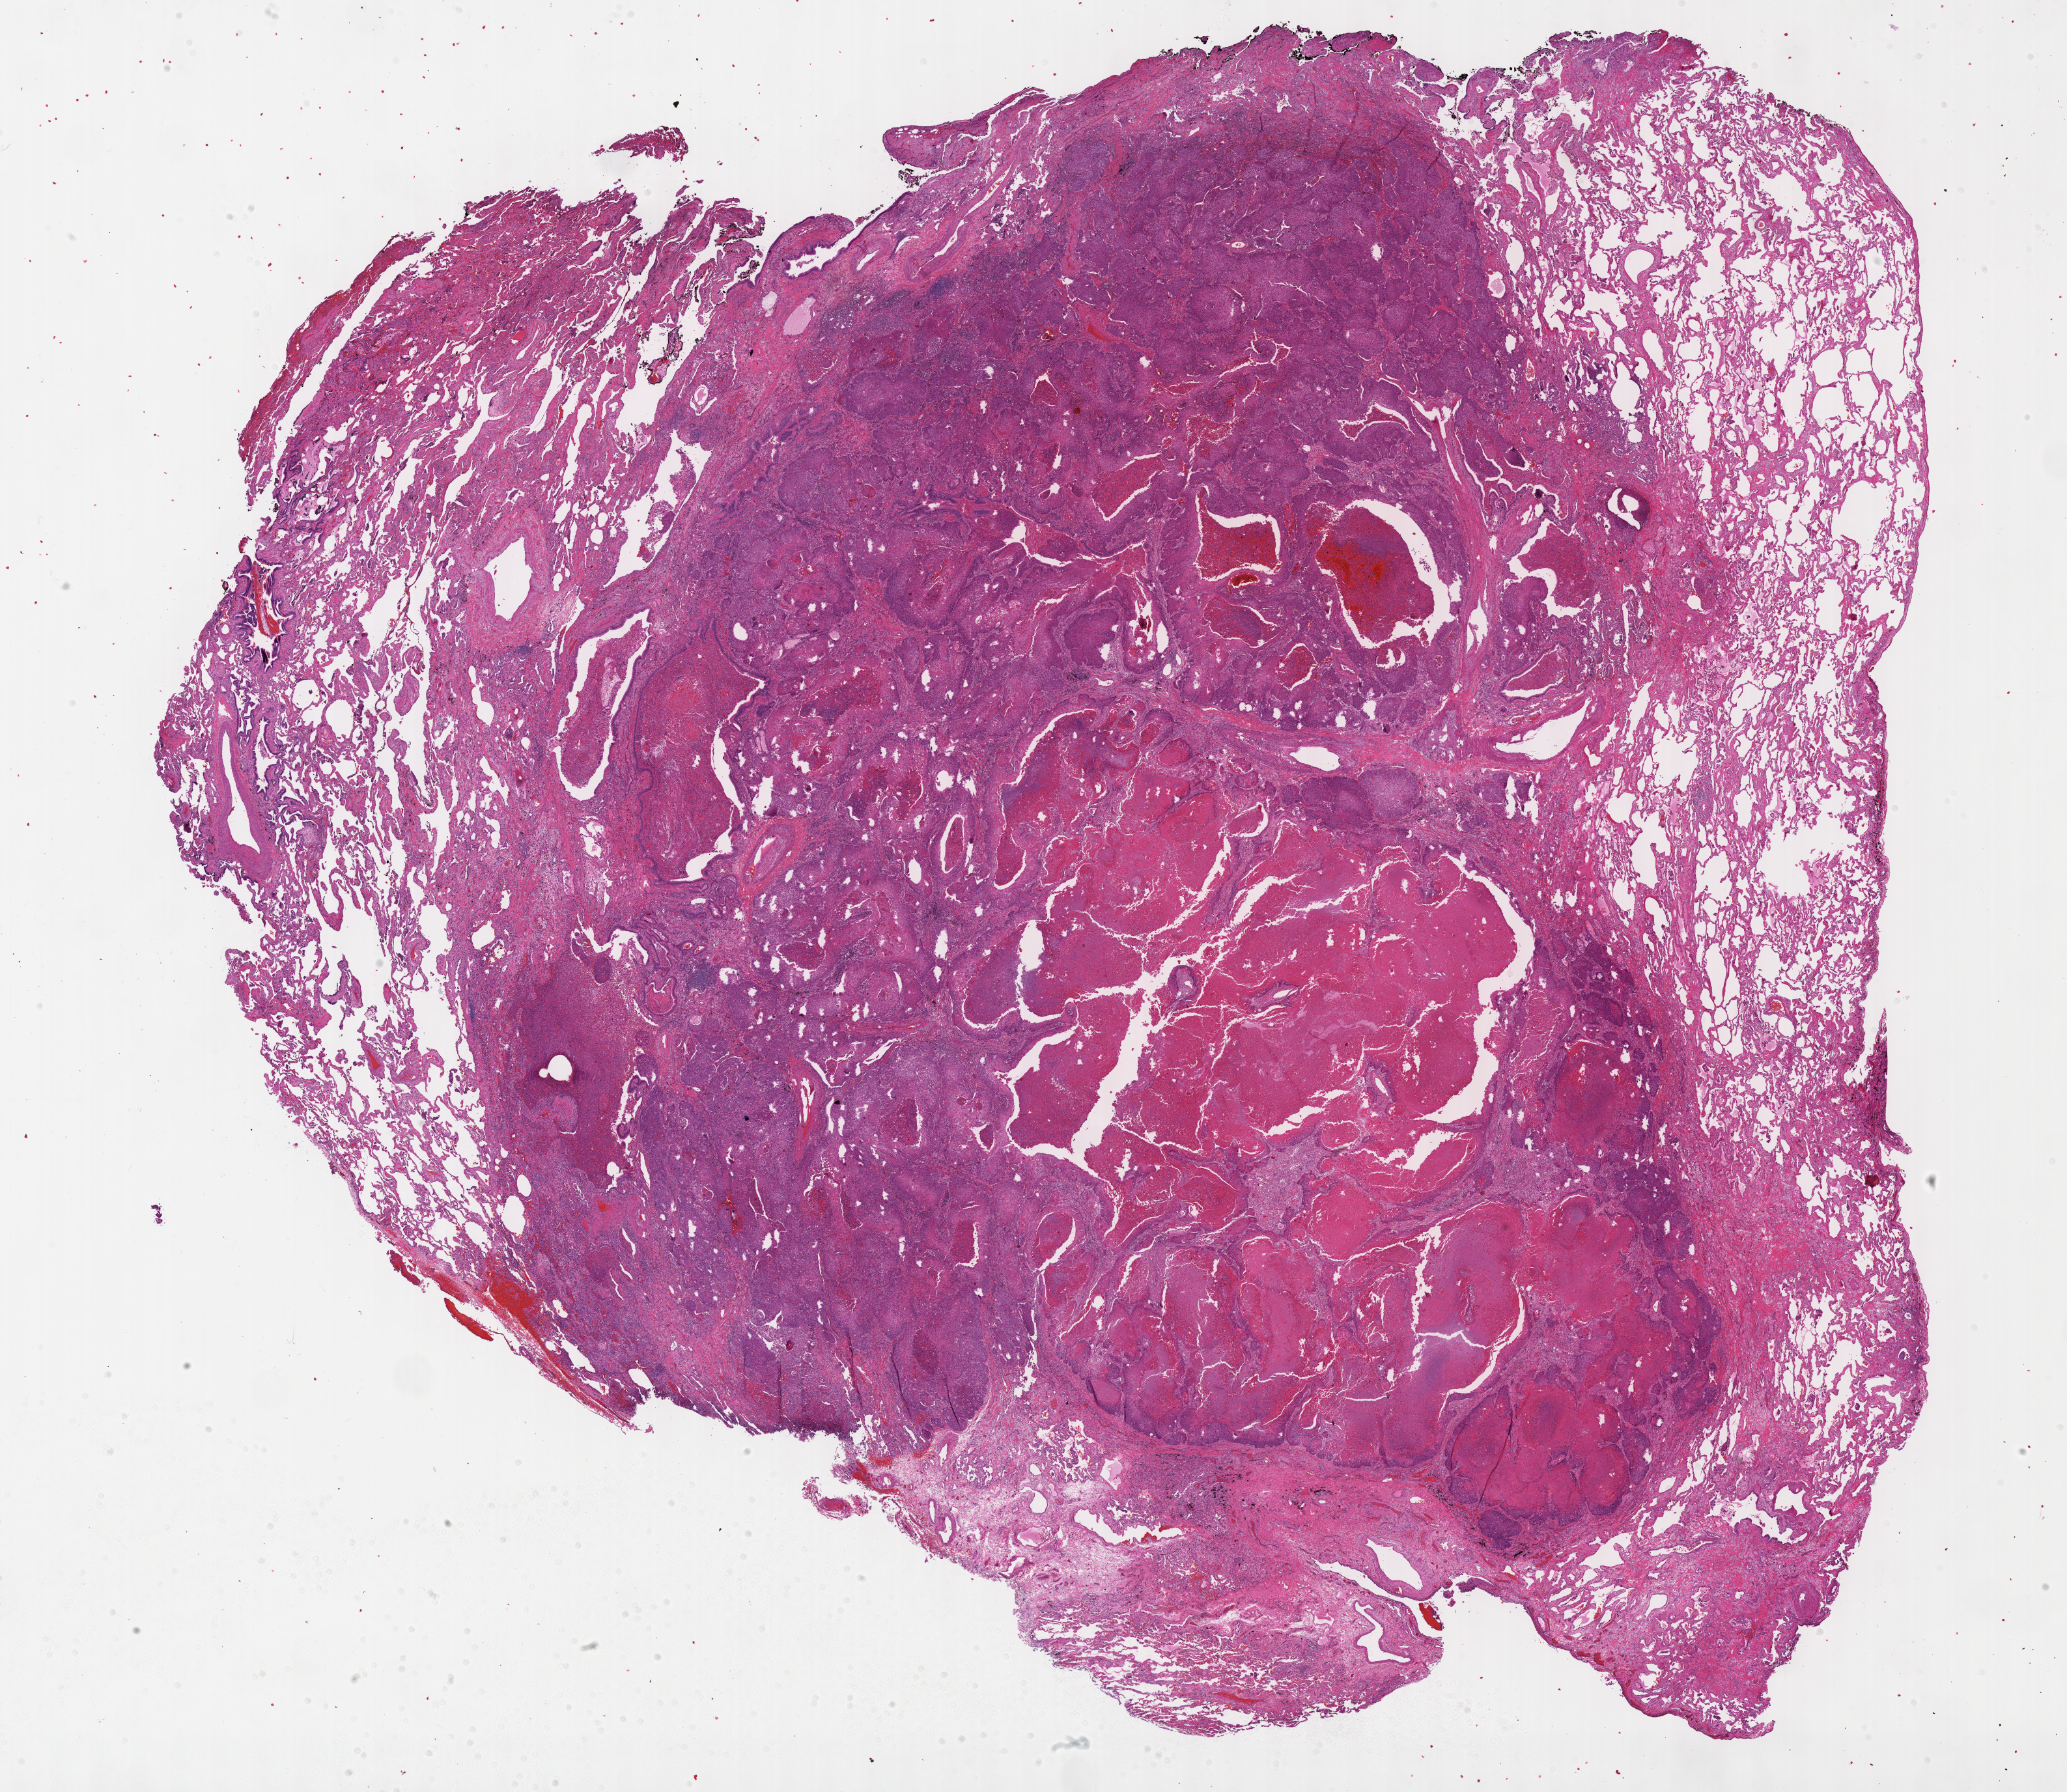
H&E-stained whole-slide image, shown as a low-resolution overview of the whole scanned area (about 25.7 x 22.3 mm); formalin-fixed paraffin-embedded (FFPE) diagnostic section; sample: primary tumour, lung. Male, age 67 years at initial diagnosis.
* laterality: right
* AJCC pathologic stage: IIA (7th edition)
* diagnosis: Squamous cell carcinoma, NOS (lower lobe, lung)